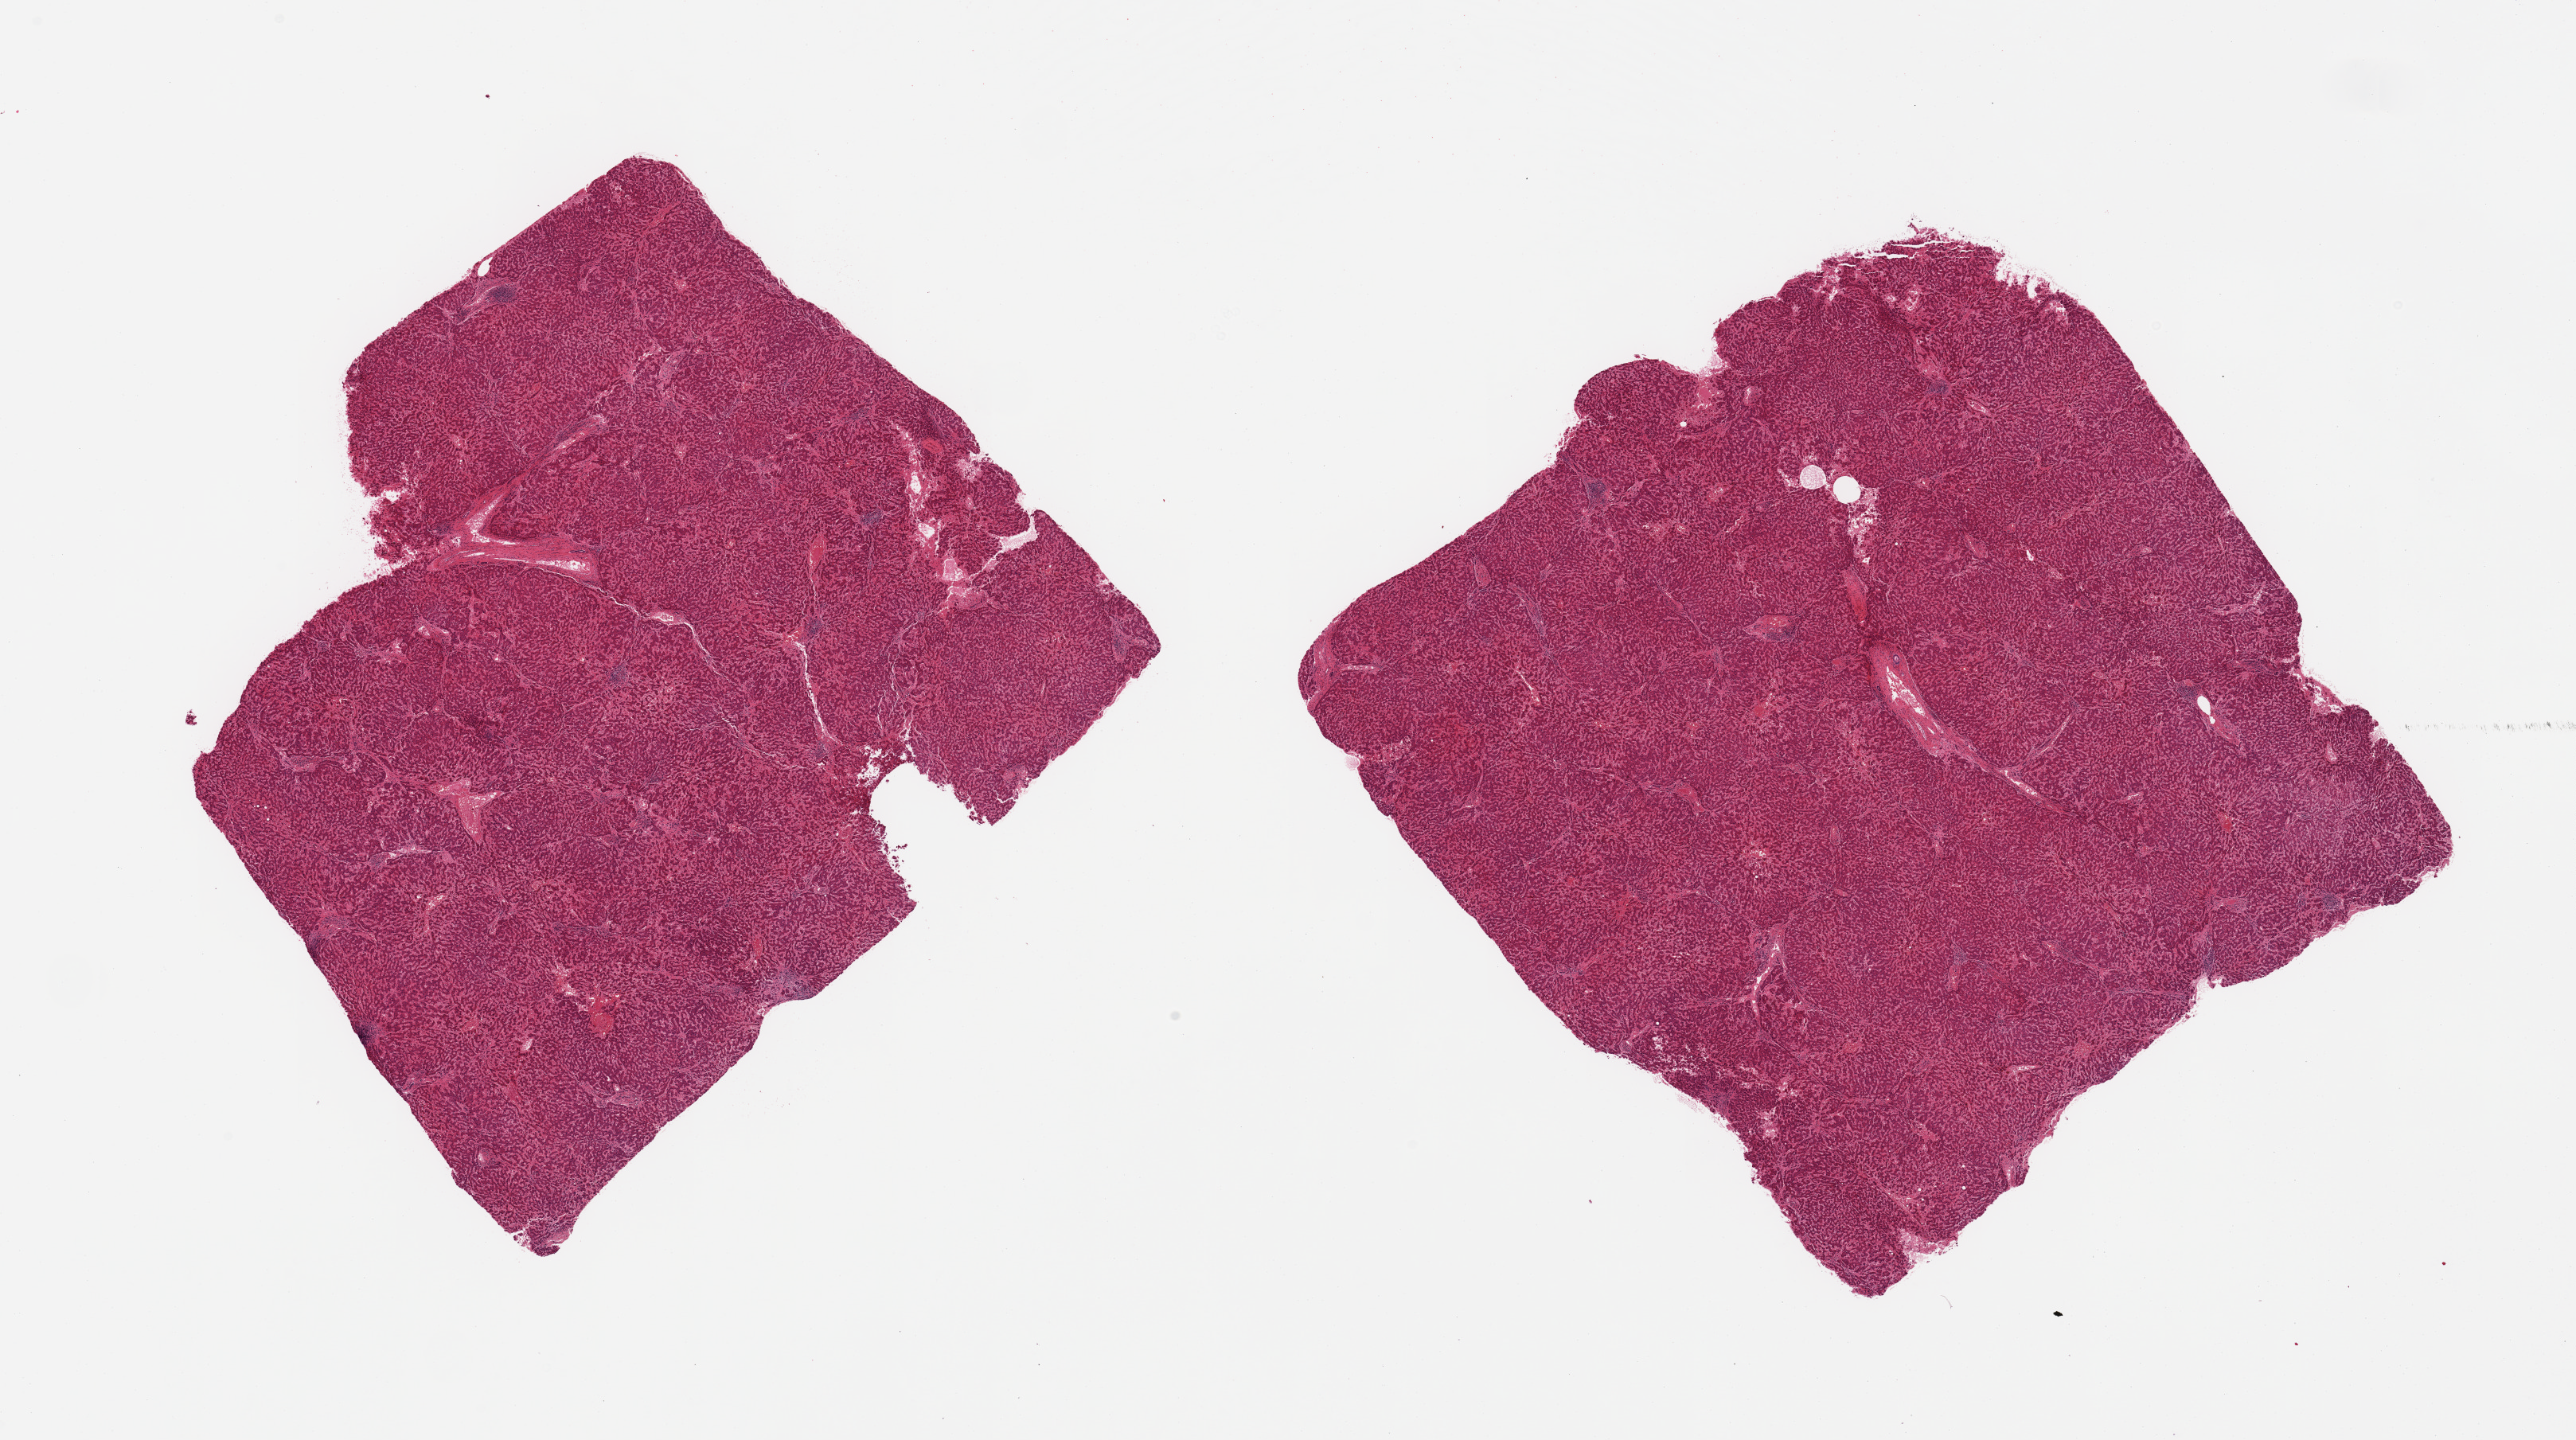
Haematoxylin and eosin whole-slide image — a low-resolution overview of the entire scanned area, about 25.6 x 14.3 mm. PAXgene-fixed paraffin-embedded (PFPE) section. Section of liver (target tissue). Donor tissue sample.
• reviewer comment on this tissue sample: 2 pieces; congestion, mild fibrosis and inflammation